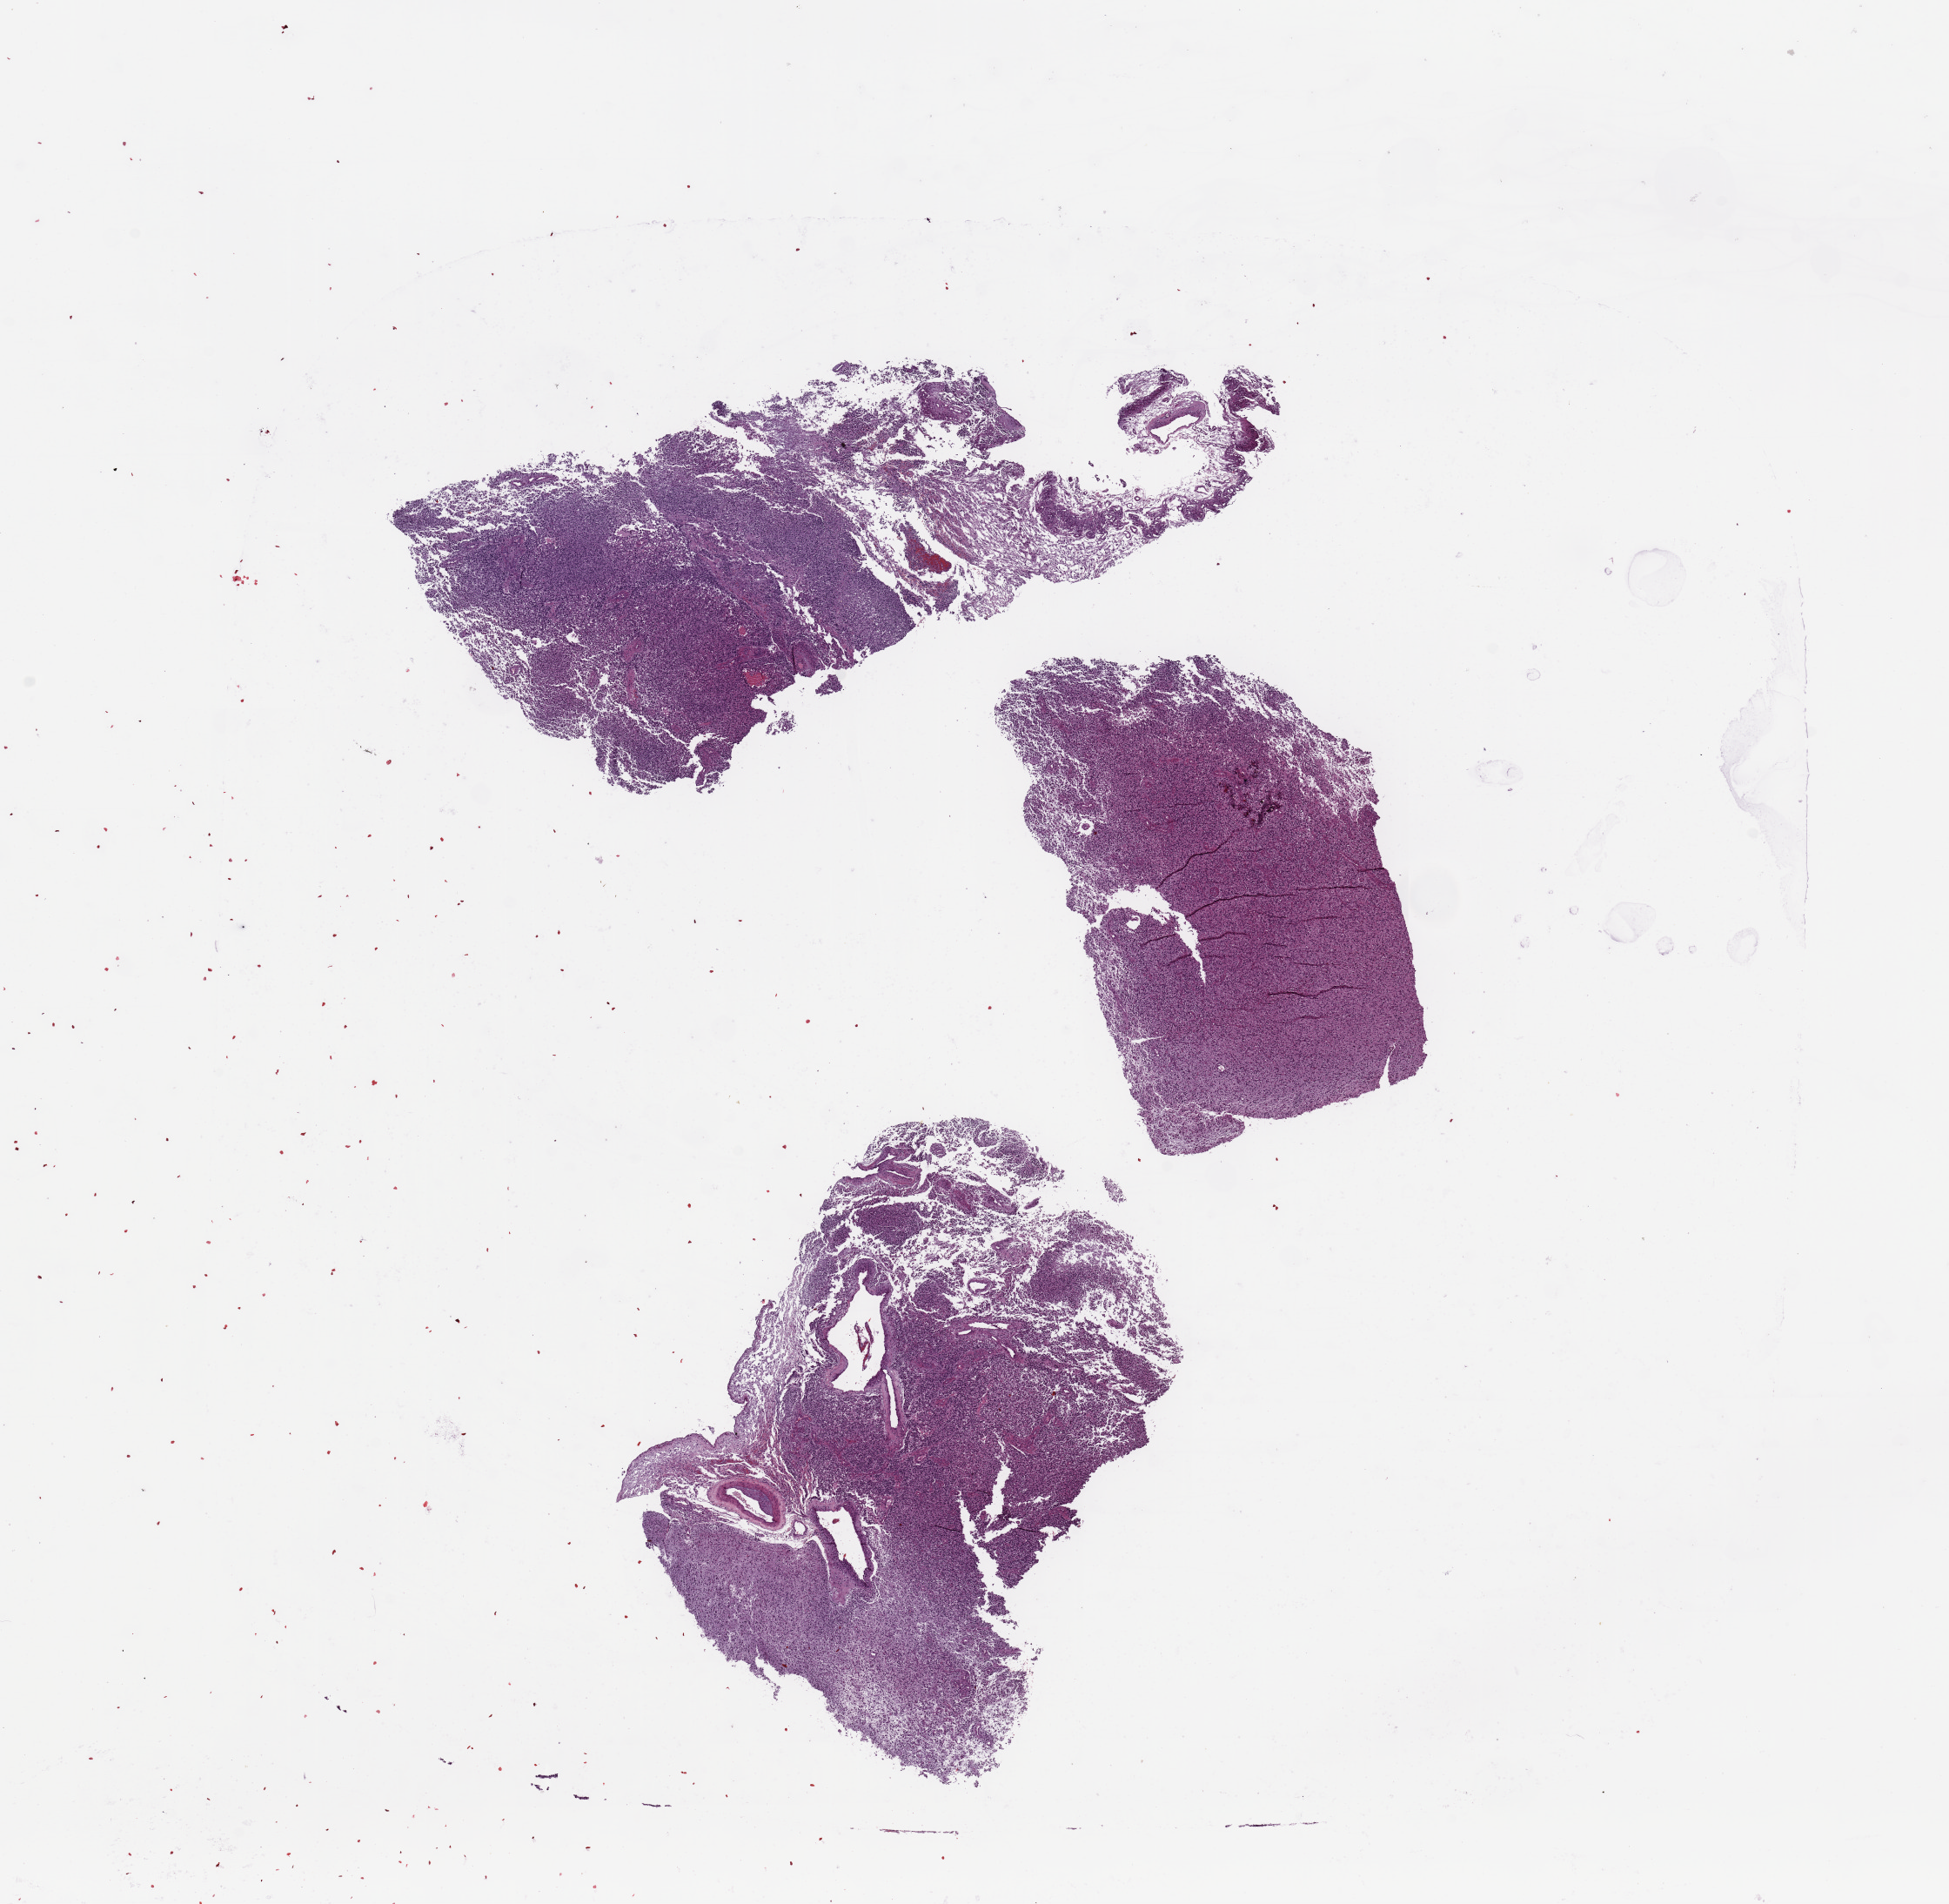
H&E-stained whole-slide image, a low-resolution overview of the entire scanned area, about 17.7 x 17.3 mm. Tumour tissue sample, sampled site: frontal lobe. 70-year-old male patient.
Histologic diagnosis: Glioblastoma.